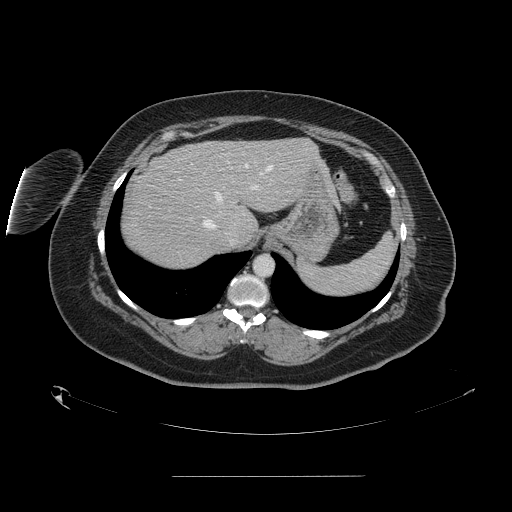
Contrast-enhanced abdominal CT, one axial slice. Slice 121 of 164 in the series (ordered by position). 120 kVp. Intravenous contrast given. Soft-tissue window (W 400 / L 40 HU). 512 × 512 image matrix. Female patient, age 52 years. From the clinical record (not read from this slice): diagnosis: colorectal cancer liver metastases, imaged before liver resection; multiple liver metastases: yes; largest metastasis: 3.5 cm; disease in both lobes: no.
Structures marked on this image (expert manual segmentation):
- hepatic veins: bounding box (x1, y1, x2, y2) in pixels: (203, 164, 272, 229)
- liver: (121, 139, 314, 269)
- planned liver remnant (the part of the liver to remain after resection): (169, 138, 314, 224)
- portal vein (with intrahepatic branches): (178, 178, 257, 189)